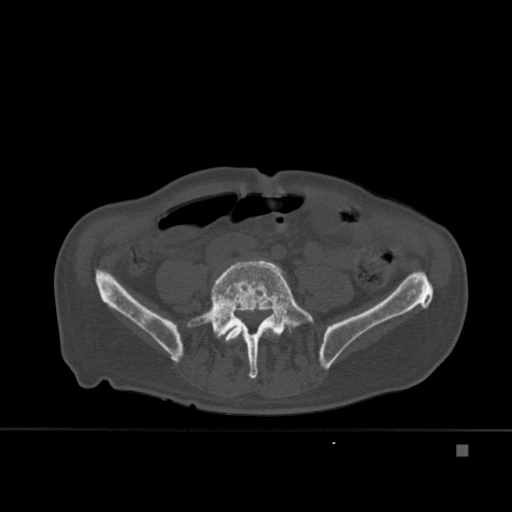
CT including the spine, one axial slice. Bone window (W 1800 / L 400 HU). 1.5 mm slice thickness. 512 × 512 image matrix, field of view 378 × 378 mm. Patient: male, 75 years. Case-level facts recorded for this patient, not image findings: primary cancer: prostate.
Structures marked on this image (semi-automatic segmentation, software-assisted and operator-edited):
- L4 vertebra: bounding box [x1, y1, x2, y2] px = [224, 325, 277, 379]
- L5 vertebra: [187, 259, 314, 379]
- T7 vertebra: [235, 316, 272, 325]